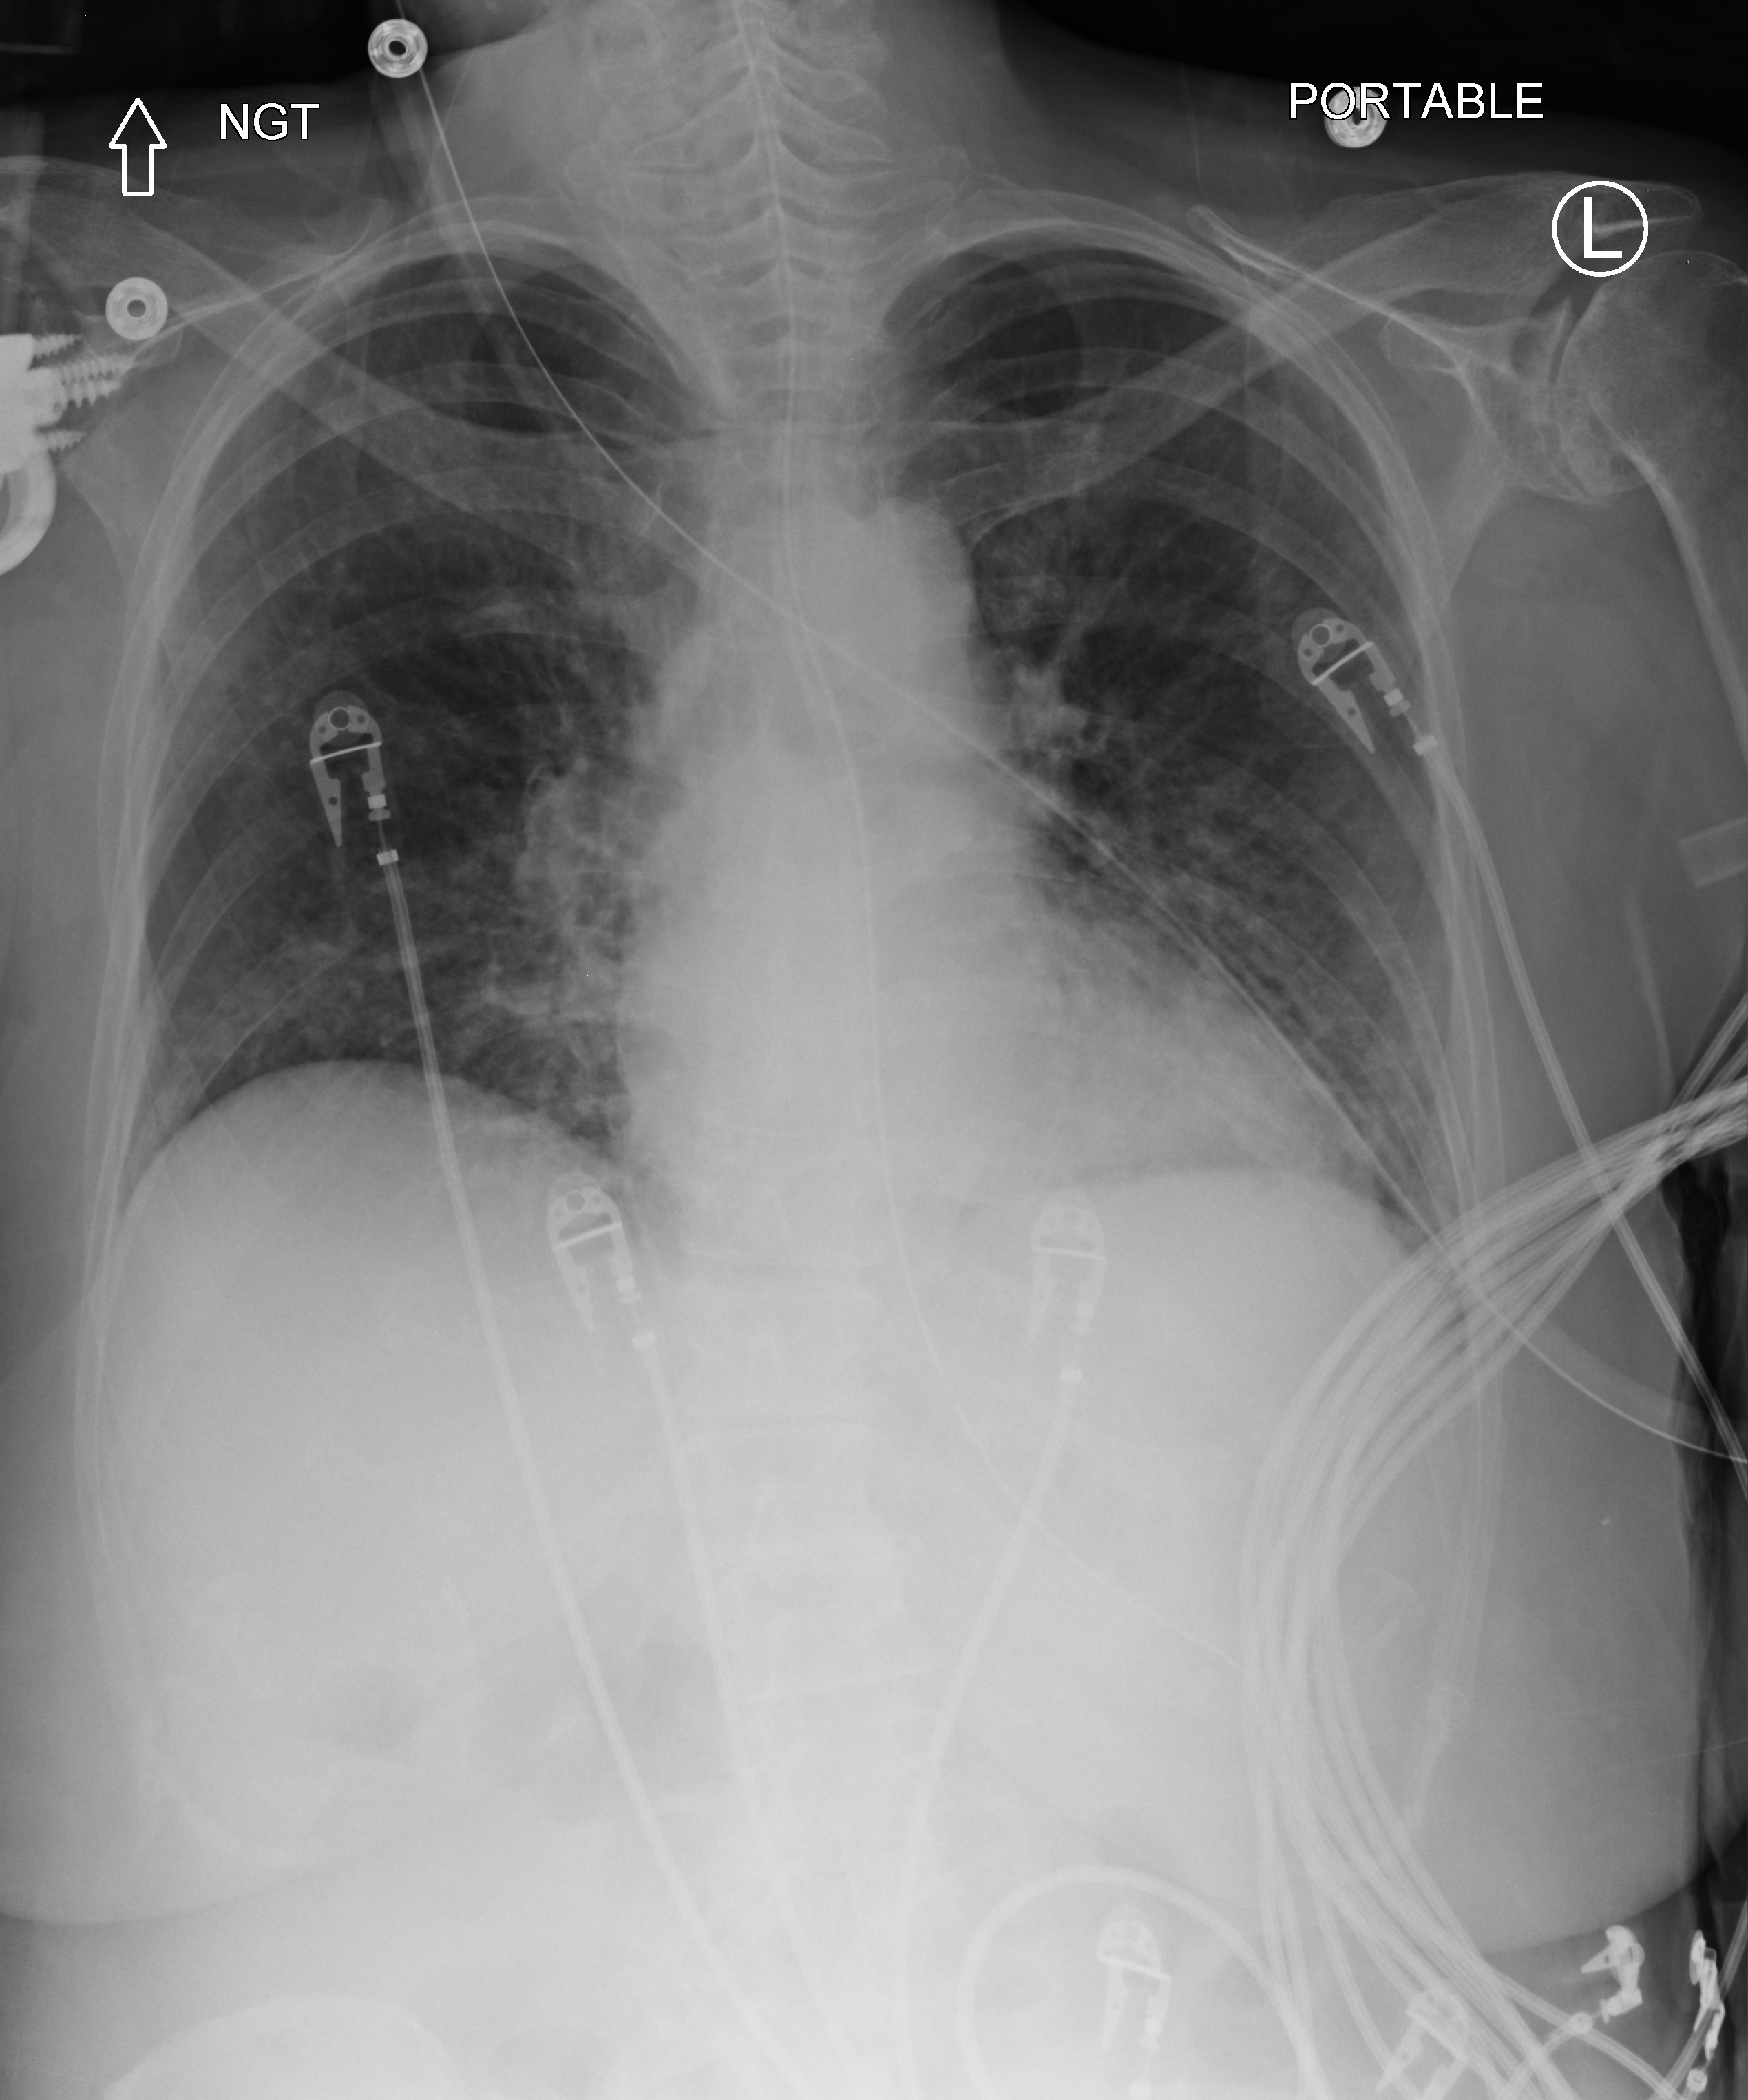
Chest X-ray (portable), anteroposterior (AP) projection. Patient hospitalised with COVID-19; female, aged 60–74 years.
Admission-level facts for this patient (not findings on this image; timing relative to this image not recorded):
- mechanically ventilated during this hospital stay: yes